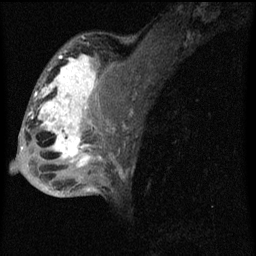
Breast MRI (dynamic contrast-enhanced), one sagittal slice. Dynamic contrast-enhanced series, image 2 of 4 at this slice position (ordered by acquisition). 1.5 T. TE 4.2 ms, TR 8 ms. 2 mm slice thickness. 256 × 256 image matrix, field of view 180 × 180 mm. Patient: female, 50 years.
Annotated regions visible in this slice (semi-automatic segmentation, software-assisted and operator-edited):
- analysis volume of interest (the breast-tissue region the enhancement analysis was run in; not a lesion): box from (x=26, y=44) to (x=124, y=177) px
- tumour enhancement mask (voxels above the 70 % enhancement threshold inside the analysis volume of interest): (x=29, y=52)–(x=108, y=167)